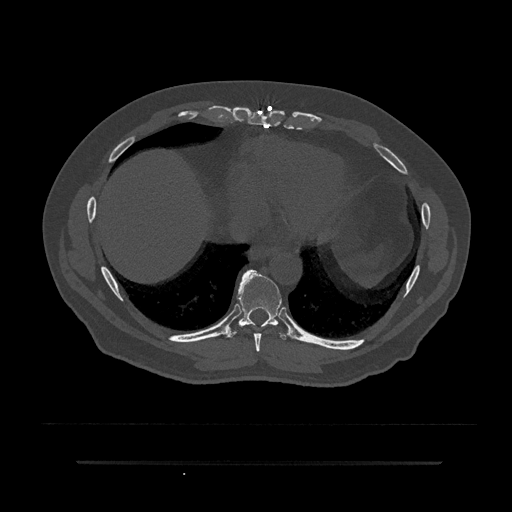
CT including the spine, one axial slice; position 396 of 797 along the scan axis; bone window (W 1800 / L 400 HU); 512 × 512 image matrix. Patient: male, 59 years. From the clinical record (not read from this slice): primary cancer: bile ducts.
Structures marked on this image (semi-automatically segmented with operator editing):
- T8 vertebra: bounding box [x1, y1, x2, y2] px = [254, 333, 262, 352]
- T9 vertebra: [226, 269, 289, 340]